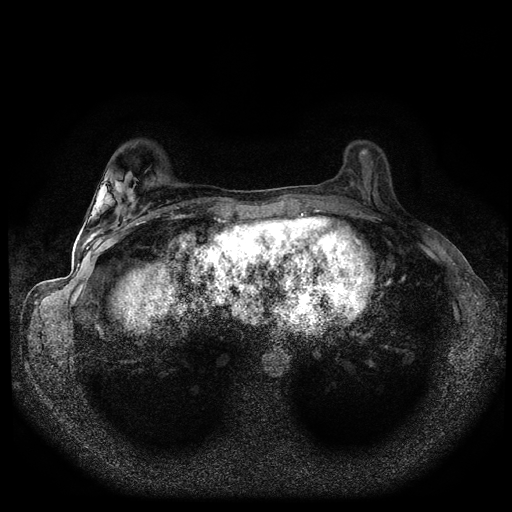
Breast MRI (dynamic contrast-enhanced, multi-phase), one axial slice. Slice 32 of 108 in the series (ordered by position). Dynamic contrast-enhanced series, time point 2 of 5 at this slice position (early post-contrast). 1.5 T. TE 2.7 ms, TR 5.5 ms. 512 × 512 image matrix, field of view 320 × 320 mm. Female patient, age 36 years.
Annotated regions visible in this slice (semi-automatically segmented with operator editing):
- breast lesion (labelled benign in the annotation): bounding box [x1, y1, x2, y2] px = [108, 171, 139, 205]